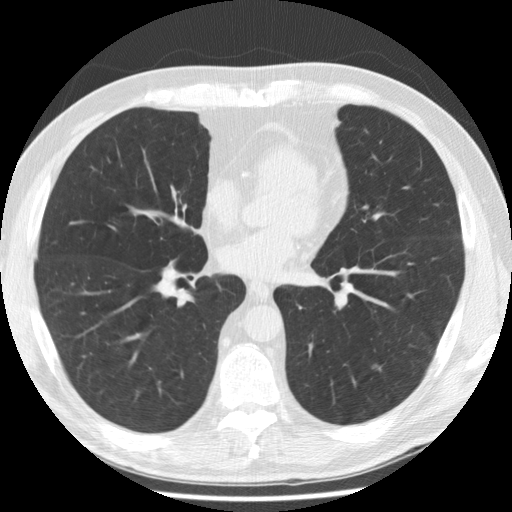
Chest CT (low-dose screening protocol), one axial image; second annual screen; lung window (W 1500 / L -600 HU); standard (soft-tissue) reconstruction kernel (STANDARD); 512 × 512 image matrix, field of view 350 × 350 mm. Male, age 58 years at enrolment. Former smoker at enrolment.
Expert-annotated lung lesion, bounding box (x1, y1, x2, y2) in pixels: (357, 351, 396, 384). Screening reader's record for this exam (one nodule recorded; not confirmed to be the boxed lesion): non-calcified nodule or mass ≥4 mm, left lower lobe, 7 × 4 mm, poorly defined margins, ground glass attenuation, pre-existing on the prior screen: yes; interval growth: yes. Lung cancer was diagnosed 407 days after this screen: adenocarcinoma, NOS, left lower lobe, poorly differentiated (G3), stage IA (AJCC 6th edition), 8 mm at pathology.